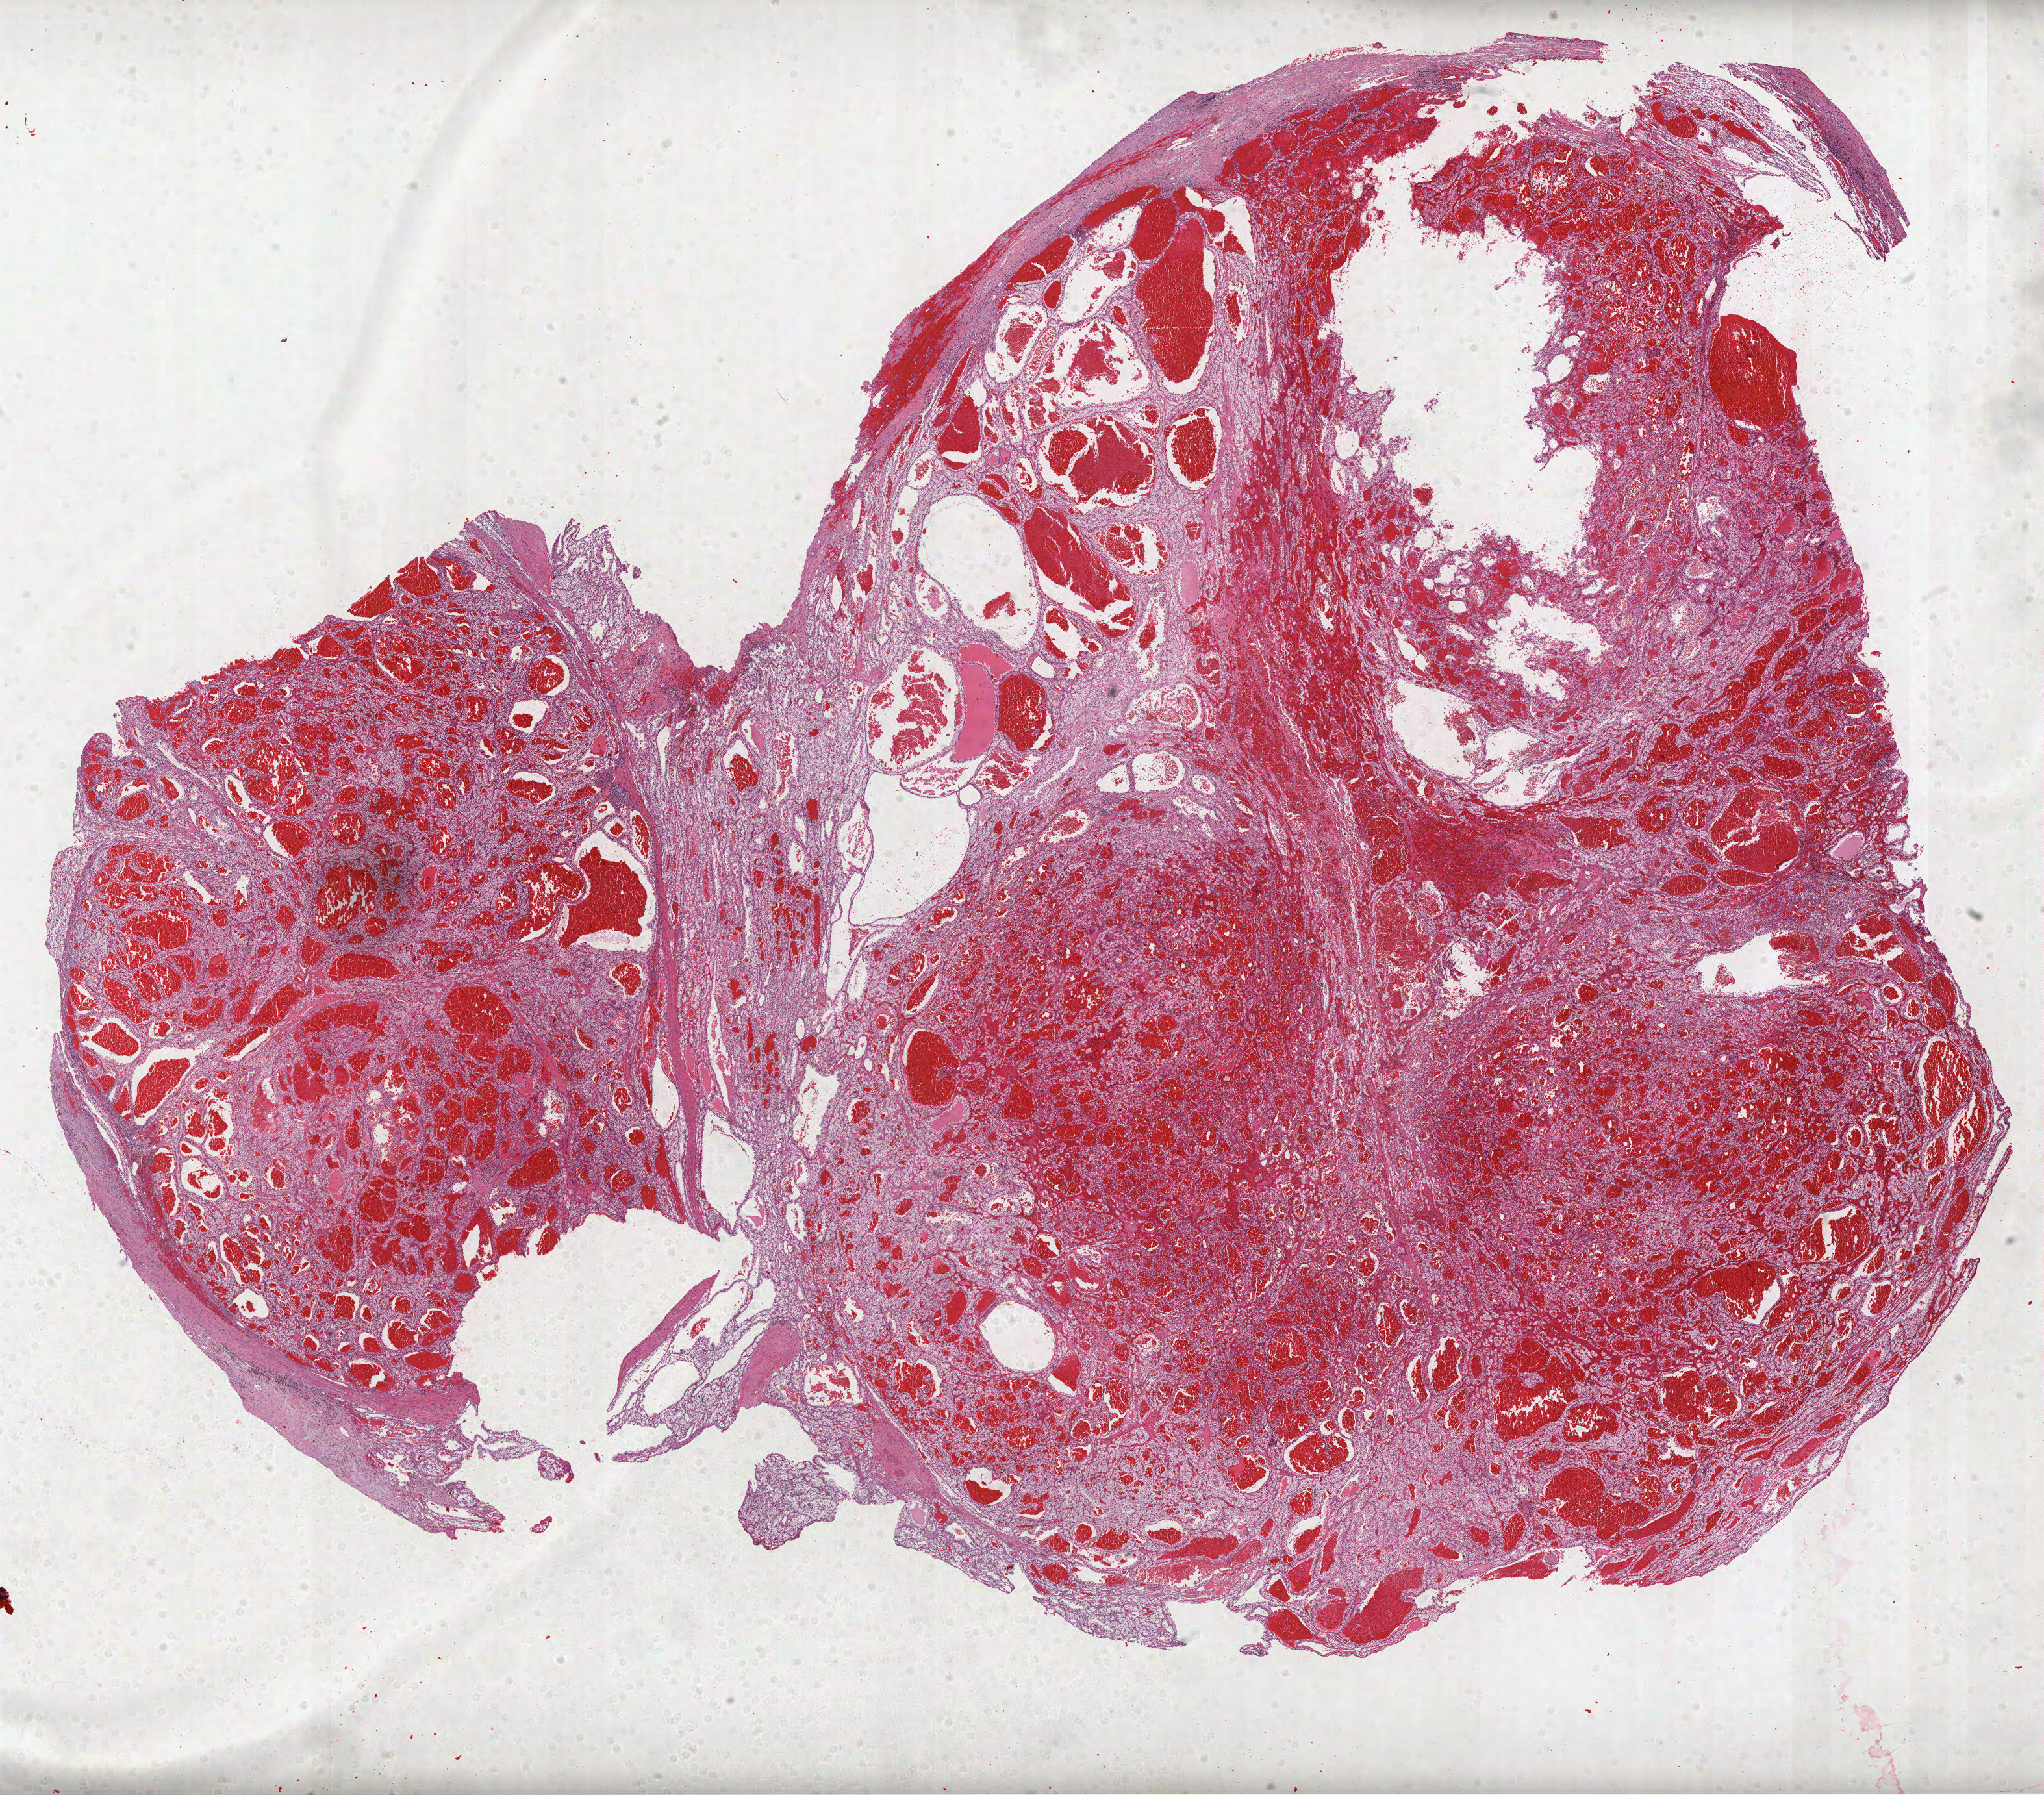
Hematoxylin and eosin (H&E) stained whole-slide image — a low-resolution overview of the entire scanned area, about 25.4 x 22.3 mm (from a 40x scan). FFPE section. Sample: primary tumour, kidney. Patient: male, age at initial diagnosis 88 years. Histologic grade: G2 (moderately differentiated).
- histologic diagnosis: Clear cell adenocarcinoma, NOS
- AJCC pathologic stage: I